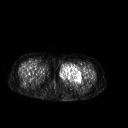
FDG PET of an extremity soft-tissue mass (from a PET/CT study), one axial slice. Slice 242 of 267 in the series (ordered by position). 3.27 mm slice thickness. 128 × 128 image matrix, field of view 500 × 500 mm. Patient: female, 42 years. Case-level facts recorded for this patient, not image findings: histological type: pleiomorphic leiomyosarcoma; grade: intermediate; site of the primary tumour: left thigh.
Outlined on this slice (expert contour drawn on MRI and transferred to this co-registered scan by the dataset authors):
- gross tumour volume including surrounding oedema: bounding box [x1, y1, x2, y2] px = [59, 64, 82, 83]
- gross tumour volume (mass): [59, 64, 82, 82]